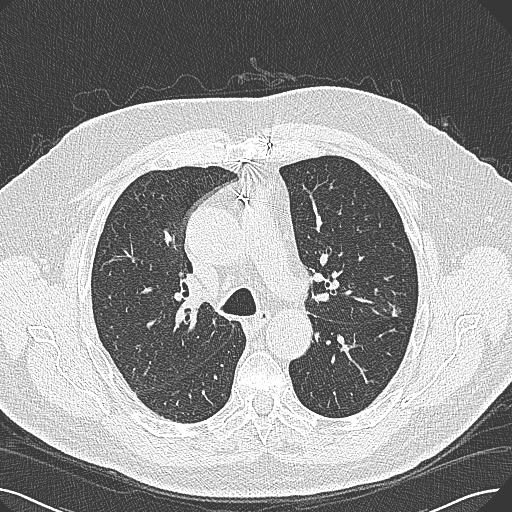
Low-dose screening chest CT, axial slice. Baseline screening round. Lung window (W 1500 / L -600 HU). Lung (sharp) reconstruction kernel (B80f). Slice 96 of 269 in the series. Male participant, aged 74 years at enrolment. Former smoker at enrolment.
Expert-annotated lung lesion, bounding box (x1, y1, x2, y2) in pixels: (363, 273, 428, 328). Screening reader's record for this exam (one nodule recorded; not confirmed to be the boxed lesion): non-calcified nodule or mass ≥4 mm, left upper lobe, 15 × 10 mm, poorly defined margins, soft tissue attenuation. Official screen result: positive, change unspecified: nodule(s) >= 4 mm or enlarging nodule(s), mass(es), or other non-specific abnormalities suspicious for lung cancer. Participant outcome: lung cancer diagnosed 124 days after this screen — adenocarcinoma, NOS, left upper lobe, well differentiated (G1), stage IA (AJCC 6th edition), 26 mm at pathology.